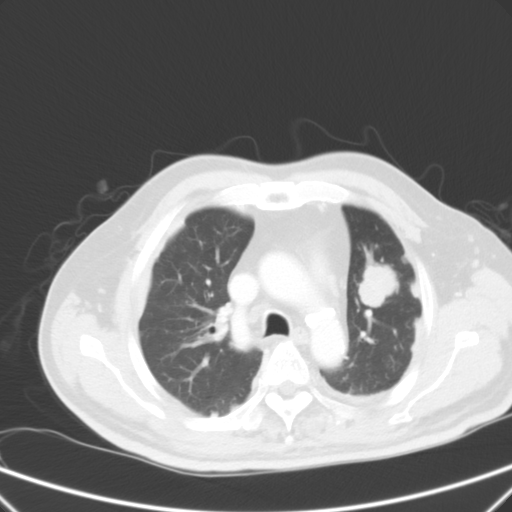
Chest CT, one axial slice; position 42 of 59 along the scan axis; 120 kVp; intravenous contrast given; lung window (W 1500 / L -600 HU); 5 mm slice thickness; 512 × 512 image matrix. Patient: male, 66 years. From the clinical record (not read from this slice): clinical TNM (as recorded): T1c N3 M1a.
Annotated regions visible in this slice (rectangle marked by the reading radiologist):
- lung tumour (recorded histology: squamous cell carcinoma): box from (x=355, y=255) to (x=404, y=311) px